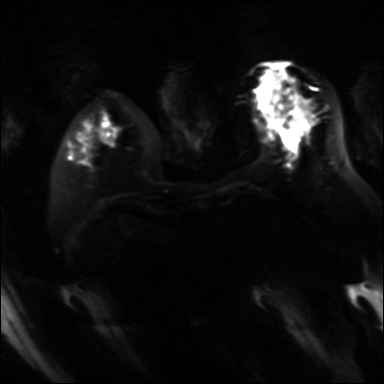
Breast MRI, one axial slice. Diffusion-weighted series; image 2 of 4 stored at this slice position (different b-values; order by instance number). 3 T. 384 × 384 image matrix, field of view 320 × 320 mm. Female patient.
Structures marked on this image (manually delineated by an expert):
- tumour on diffusion-weighted imaging: bounding box [x1, y1, x2, y2] px = [290, 117, 309, 137]